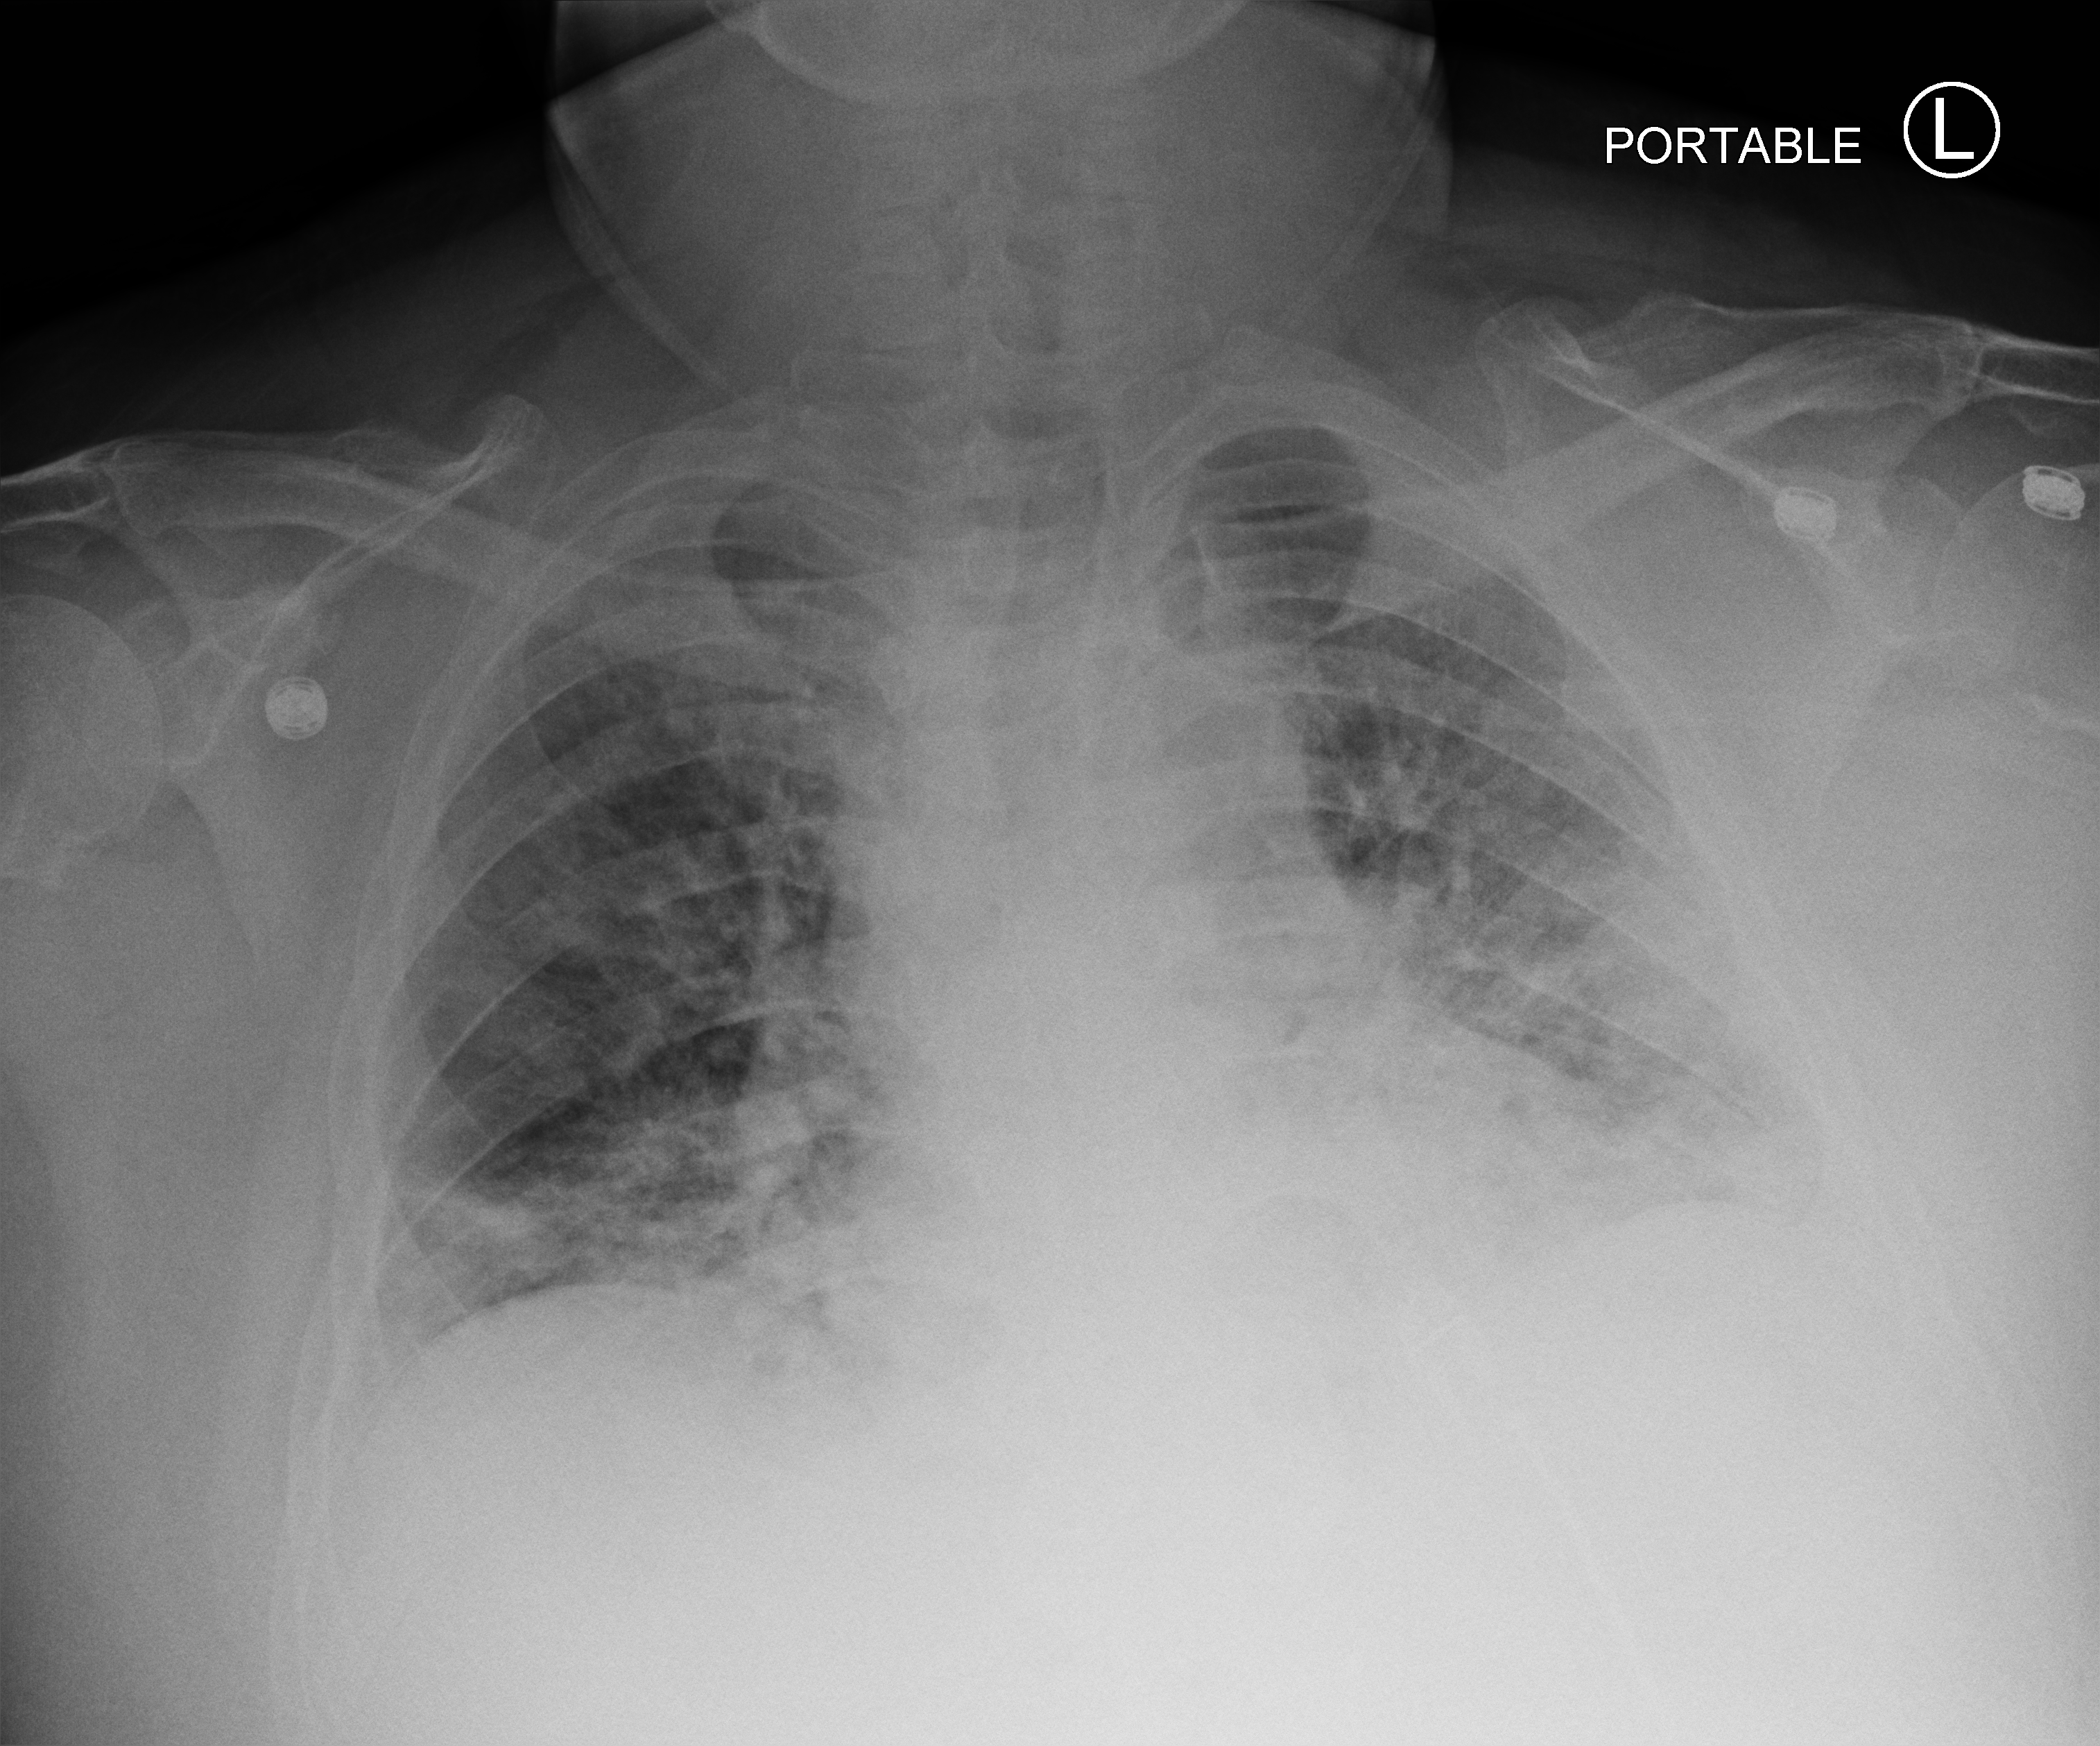
Portable chest radiograph; anteroposterior (AP) projection. Patient hospitalised with COVID-19; male, aged 18–59 years.
Admission-level facts for this patient (not findings on this image; timing relative to this image not recorded): hypertension (admission record): yes; smoking status (admission record): never.